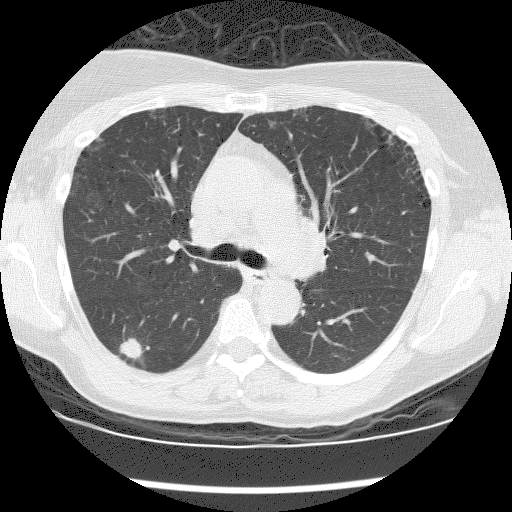
Chest CT (low-dose screening protocol), one axial image; baseline screening round; lung window (W 1500 / L -600 HU); 2.5 mm slice thickness; lung (sharp) reconstruction kernel (BONE); 120 kVp; slice 58 of 176 in the series; 512 × 512 image matrix, field of view 320 × 320 mm. Female, age 59 years at enrolment.
Expert reader's lesion annotation, bounding box (x1, y1, x2, y2) in pixels: (110, 339, 150, 371). The screening reader recorded 6 non-calcified nodules or masses ≥4 mm on this exam; which of them this box marks is not recorded. Official screen result: positive, change unspecified: nodule(s) >= 4 mm or enlarging nodule(s), mass(es), or other non-specific abnormalities suspicious for lung cancer. Lung cancer was diagnosed 242 days after this screen: adenocarcinoma, NOS, right lower lobe, moderately differentiated (G2), stage IIIA (AJCC 6th edition), 12 mm at pathology.